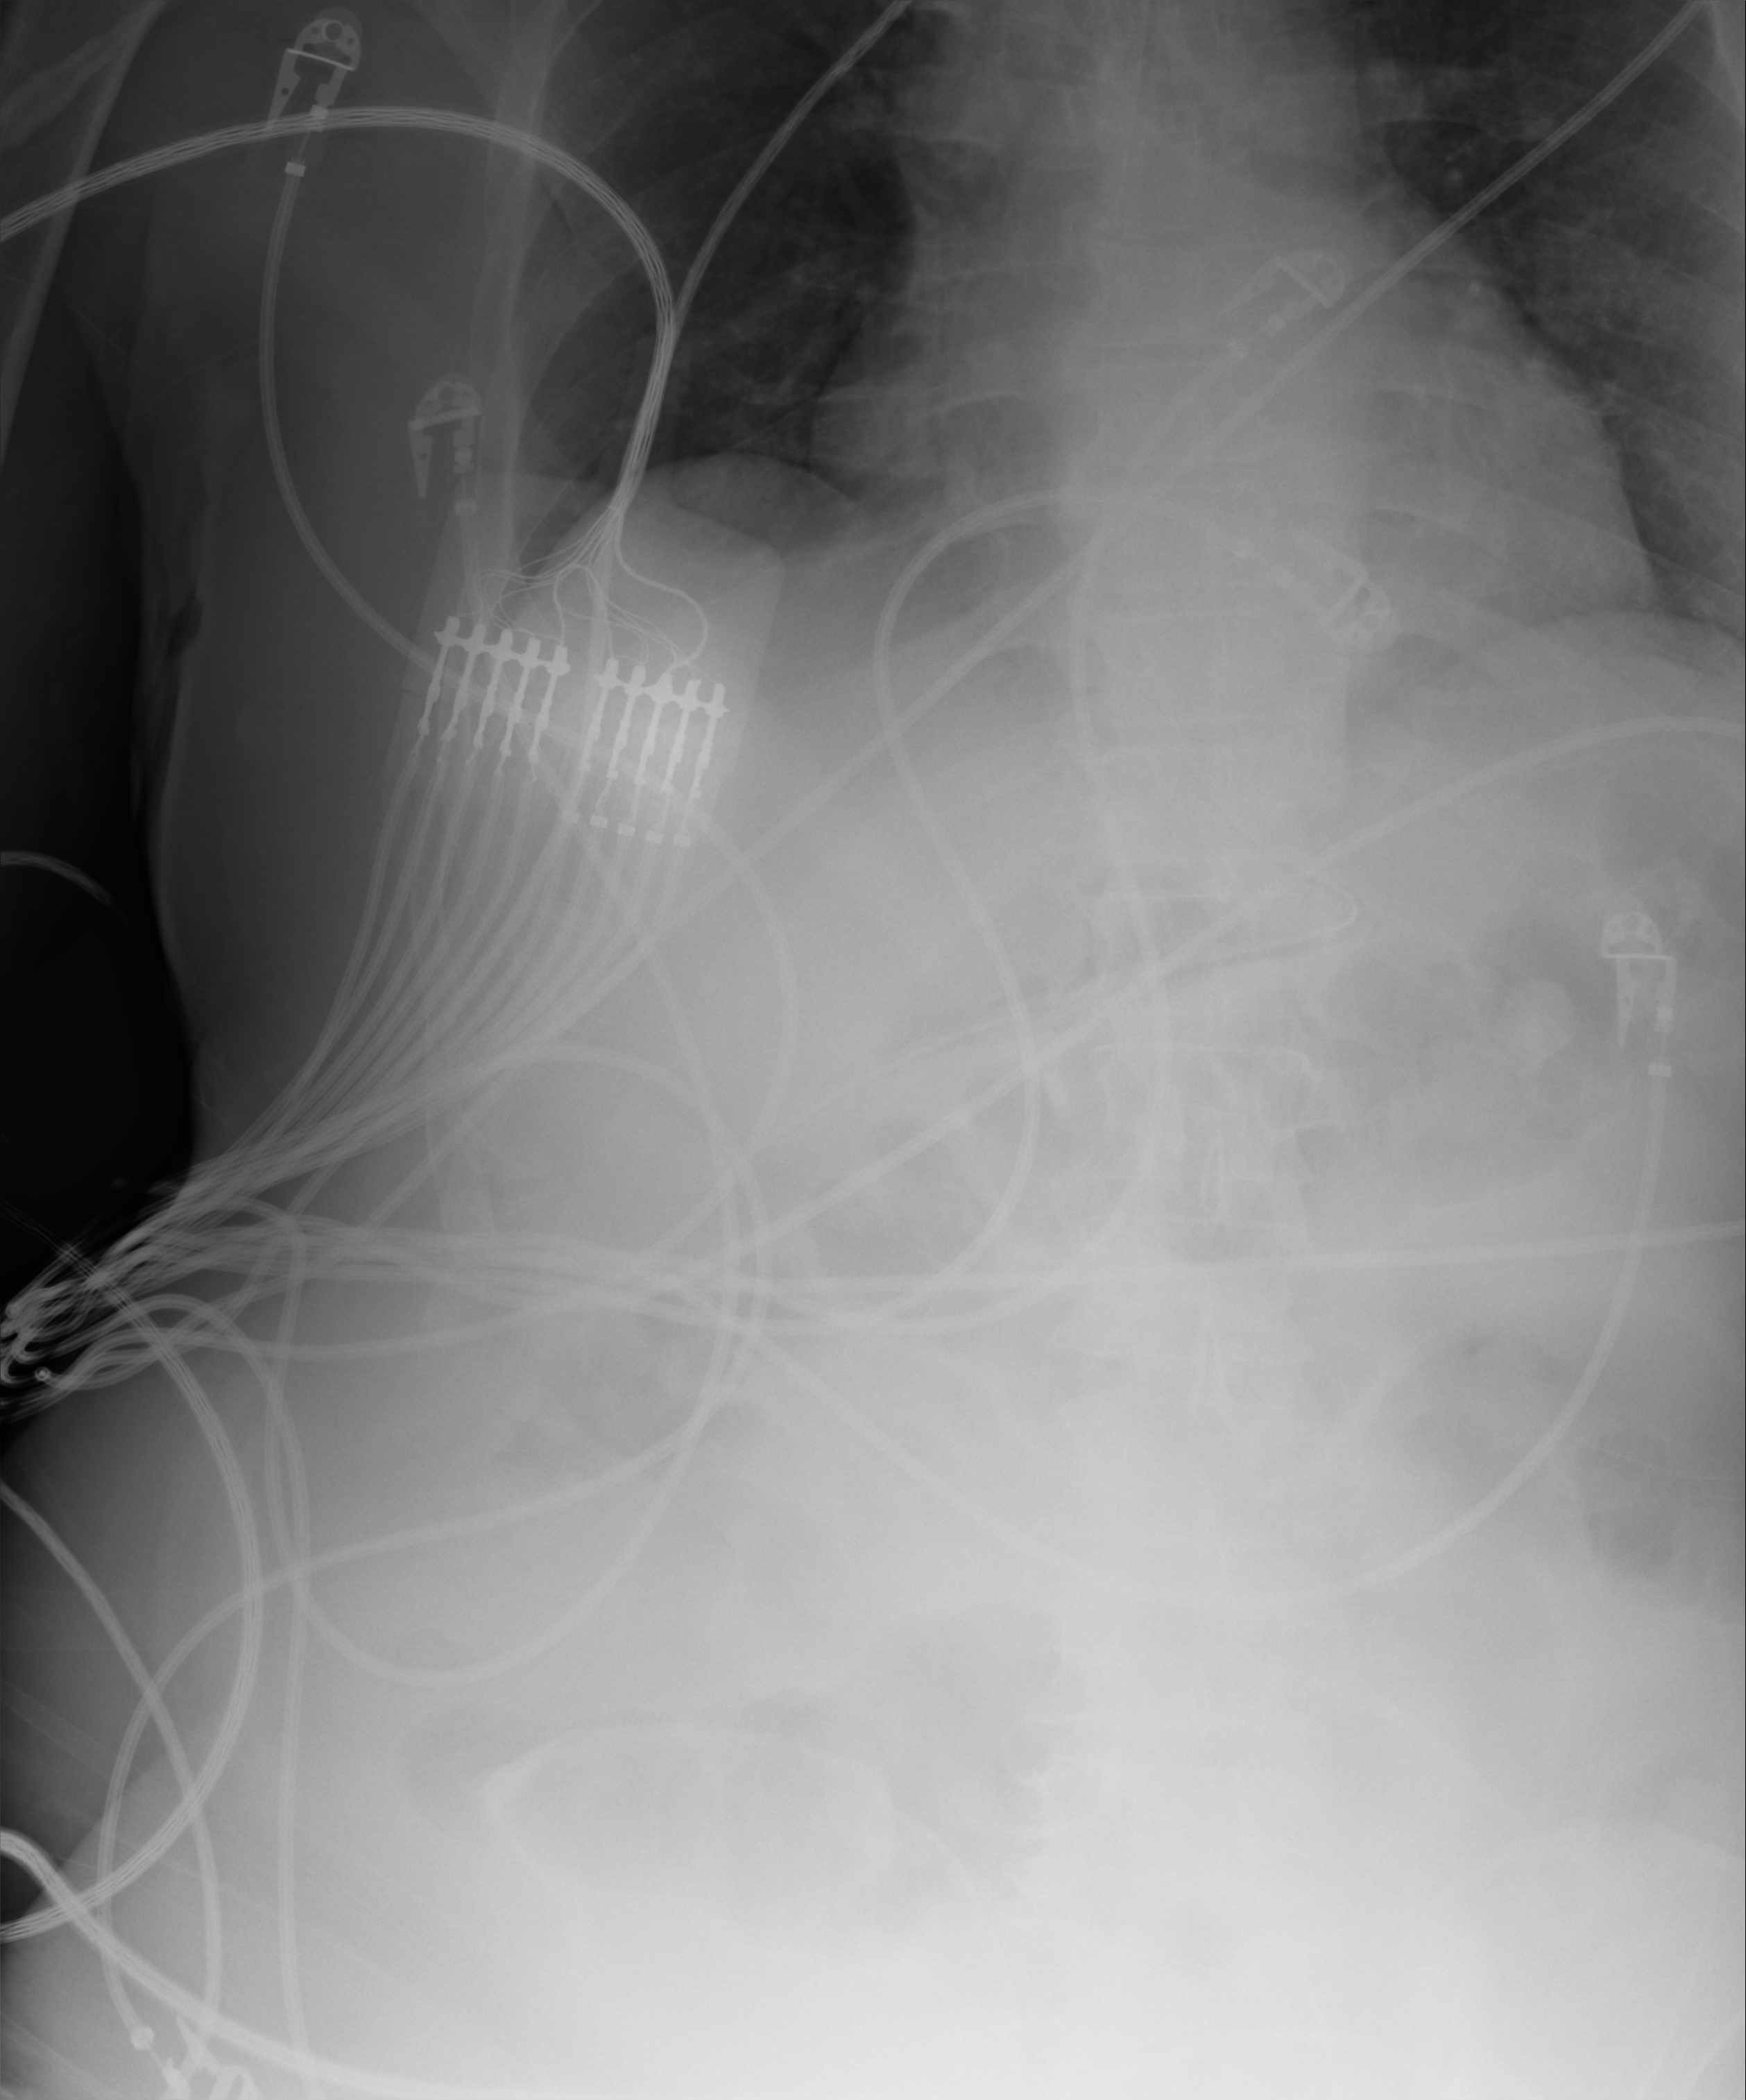
Portable chest radiograph, anteroposterior (AP) projection. Adult patient hospitalised with COVID-19, age 18–59 years.
Admission-level facts for this patient (not findings on this image; timing relative to this image not recorded):
- mechanically ventilated during this hospital stay: yes
- length of hospital stay: 37 days
- admitted to intensive care during this hospital stay: yes